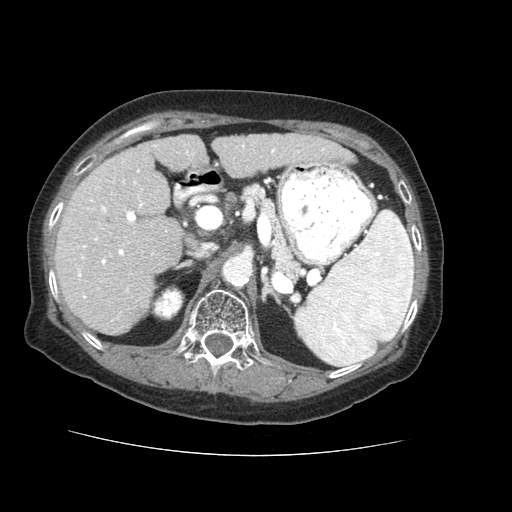
Contrast-enhanced abdominal CT (liver protocol), one axial slice. Slice 32 of 73 in the series (ordered by position). Reconstruction kernel STANDARD. Soft-tissue window (W 400 / L 40 HU). 2.5 mm slice thickness. 512 × 512 image matrix. From the clinical record (not read from this slice): diagnosis: hepatocellular carcinoma (patient treated with transarterial chemoembolisation; whether this scan precedes or follows treatment is not stated here); TNM stage (as recorded): Stage-IVB; Child-Pugh class: A; tumour differentiation: well differentiated.
Annotated regions visible in this slice (semi-automatic segmentation, software-assisted and operator-edited):
- liver parenchyma outside the tumour (the mass and vessels are separate outlines, so this box may not span the whole liver): box from (x=54, y=134) to (x=352, y=334) px
- liver vessels: (x=77, y=145)–(x=324, y=299)